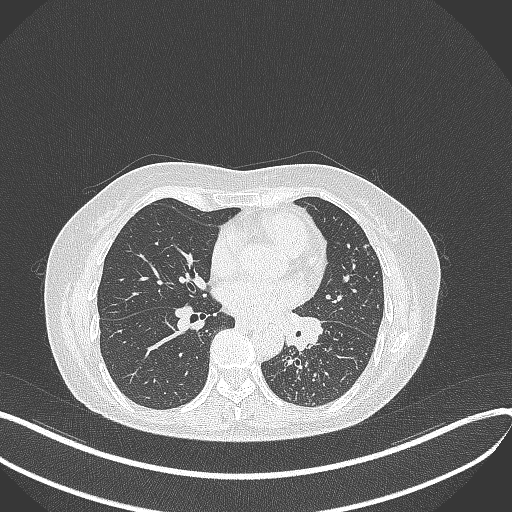
Chest CT, one axial slice; reconstruction kernel B70f; 100 kVp; lung window (W 1500 / L -600 HU); 1 mm slice thickness; 512 × 512 image matrix, field of view 400 × 400 mm. Patient: female, 63 years. Case-level facts recorded for this patient, not image findings: clinical TNM (as recorded): T1b N0 M0; histopathological grade: G2-3.
Structures marked on this image (bounding box drawn by a radiologist):
- lung tumour (recorded histology: adenocarcinoma): bounding box [x1, y1, x2, y2] px = [281, 307, 324, 353]